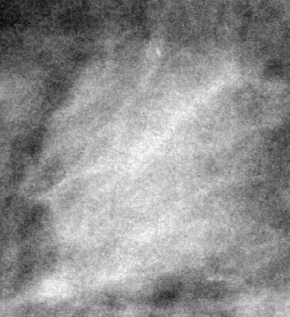
Region of interest cut from a scanned film mammogram (one marked finding); right breast; MLO view; BI-RADS breast density category 3 (scale 1–4).
Finding: mass, shape round, margins circumscribed / ill defined; BI-RADS assessment category 4; subtlety rating 4 on a 1 (subtle) to 5 (obvious) scale; pathology (as recorded): benign.